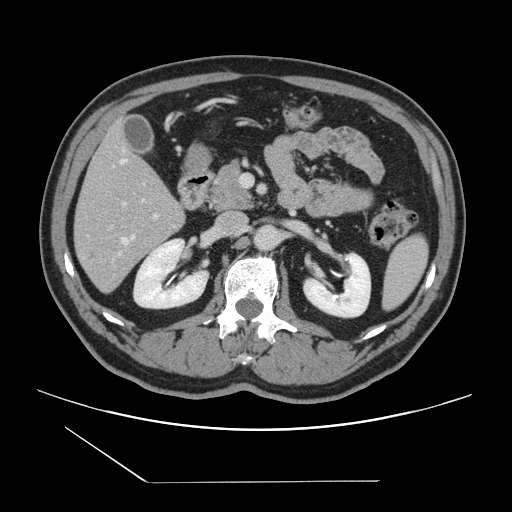
Contrast-enhanced abdominal CT, one axial slice. Slice 64 of 157 in the series (ordered by position). 120 kVp. Intravenous contrast given. Soft-tissue window (W 400 / L 40 HU). 2.5 mm slice thickness. 512 × 512 image matrix, field of view 407 × 407 mm. Male patient, age 61 years. From the clinical record (not read from this slice): diagnosis: colorectal cancer liver metastases, imaged before liver resection; multiple liver metastases: yes; largest metastasis: 5.5 cm; chemotherapy before resection: no.
Outlined on this slice (outlined manually by an expert reader):
- hepatic veins: bounding box <120,159,143,254> (left, top, right, bottom; pixels)
- liver: <75,126,184,292>
- planned liver remnant (the part of the liver to remain after resection): <76,125,174,218>
- portal vein (with intrahepatic branches): <110,203,158,228>
- liver metastasis: <88,252,105,262>